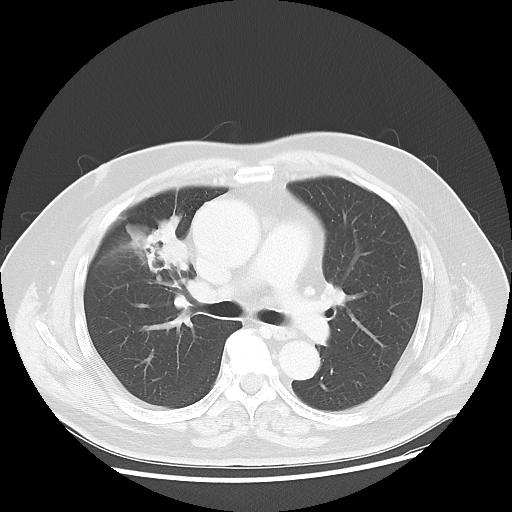
Chest CT, one axial slice; slice 27 of 48 in the series (ordered by position); reconstruction kernel LUNG; 120 kVp; lung window (W 1500 / L -600 HU); 5 mm slice thickness; 512 × 512 image matrix. Male patient, age 60 years. From the clinical record (not read from this slice): clinical TNM (as recorded): T2 N3 M0.
Annotated regions visible in this slice (bounding box drawn by a radiologist):
- lung tumour (recorded histology: adenocarcinoma): bounding box [x1, y1, x2, y2] px = [127, 207, 189, 289]